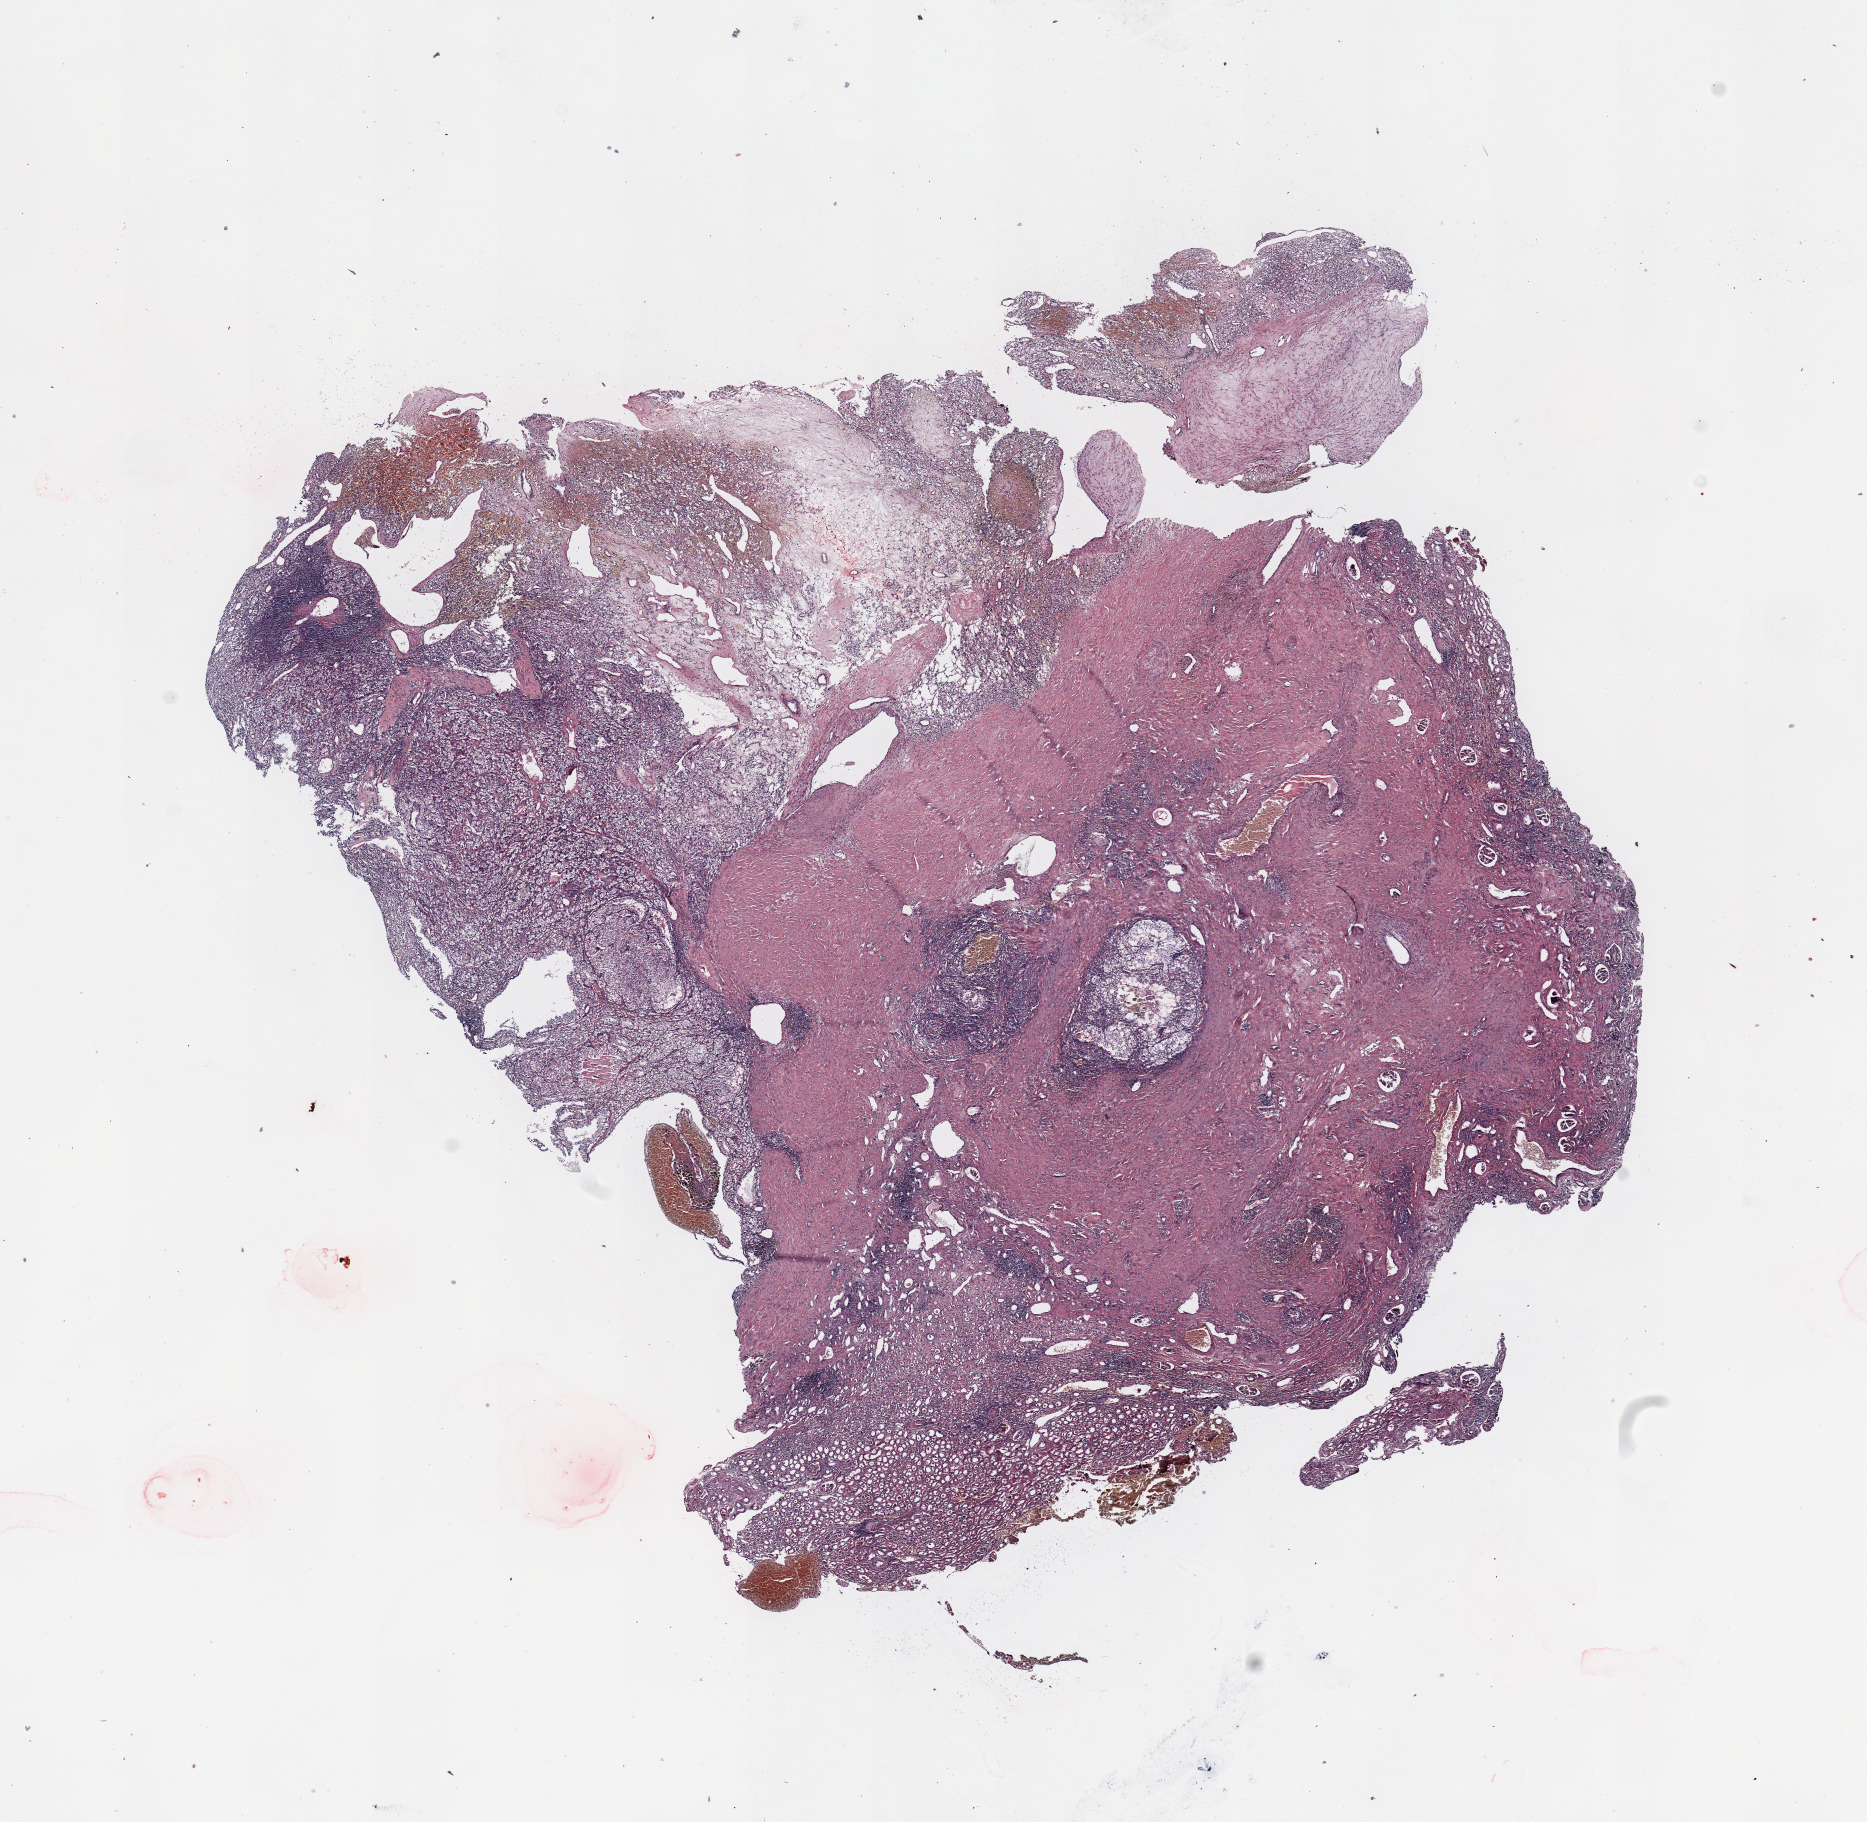
Digitized H&E tissue section (whole slide) — whole scanned area (about 14.8 x 14.4 mm) shown as a low-resolution overview, tumour tissue sample, kidney. 49-year-old male patient. Histologic grade: G2 (moderately differentiated).
Primary tumour site (as recorded): upper pole. AJCC pathologic stage: I. Histologic diagnosis: Renal cell carcinoma, NOS.